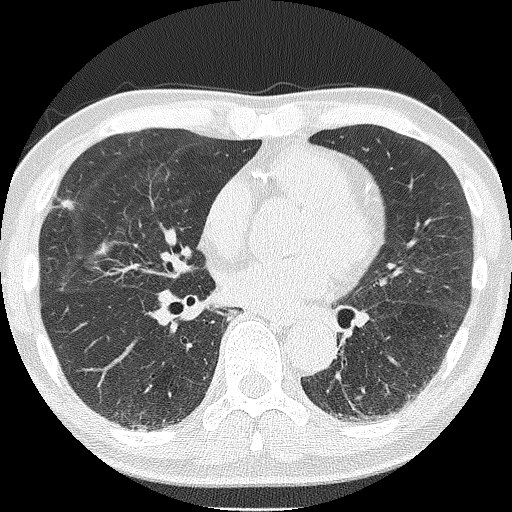
Low-dose screening chest CT, axial slice. Second screening round (one year after baseline). Lung window (W 1500 / L -600 HU). Lung (sharp) reconstruction kernel (FC51). Slice 94 of 181 in the series. 512 × 512 image matrix, field of view 287 × 287 mm. Male, age 68 years at enrolment. Current smoker at enrolment.
• Expert-annotated lung lesion, bounding box [x1, y1, x2, y2] px = [45, 186, 87, 225].
• Screening reader's record for this exam (one nodule recorded; not confirmed to be the boxed lesion): non-calcified nodule or mass ≥4 mm, right upper lobe, 6 × 4 mm, spiculated (stellate) margins, soft tissue attenuation, pre-existing on the prior screen: no.
• Official screen result: positive, other.
• Participant outcome: lung cancer diagnosed 22 days after this screen — squamous cell carcinoma, NOS, right upper lobe, moderately differentiated (G2), stage IA (AJCC 6th edition), 10 mm at pathology.